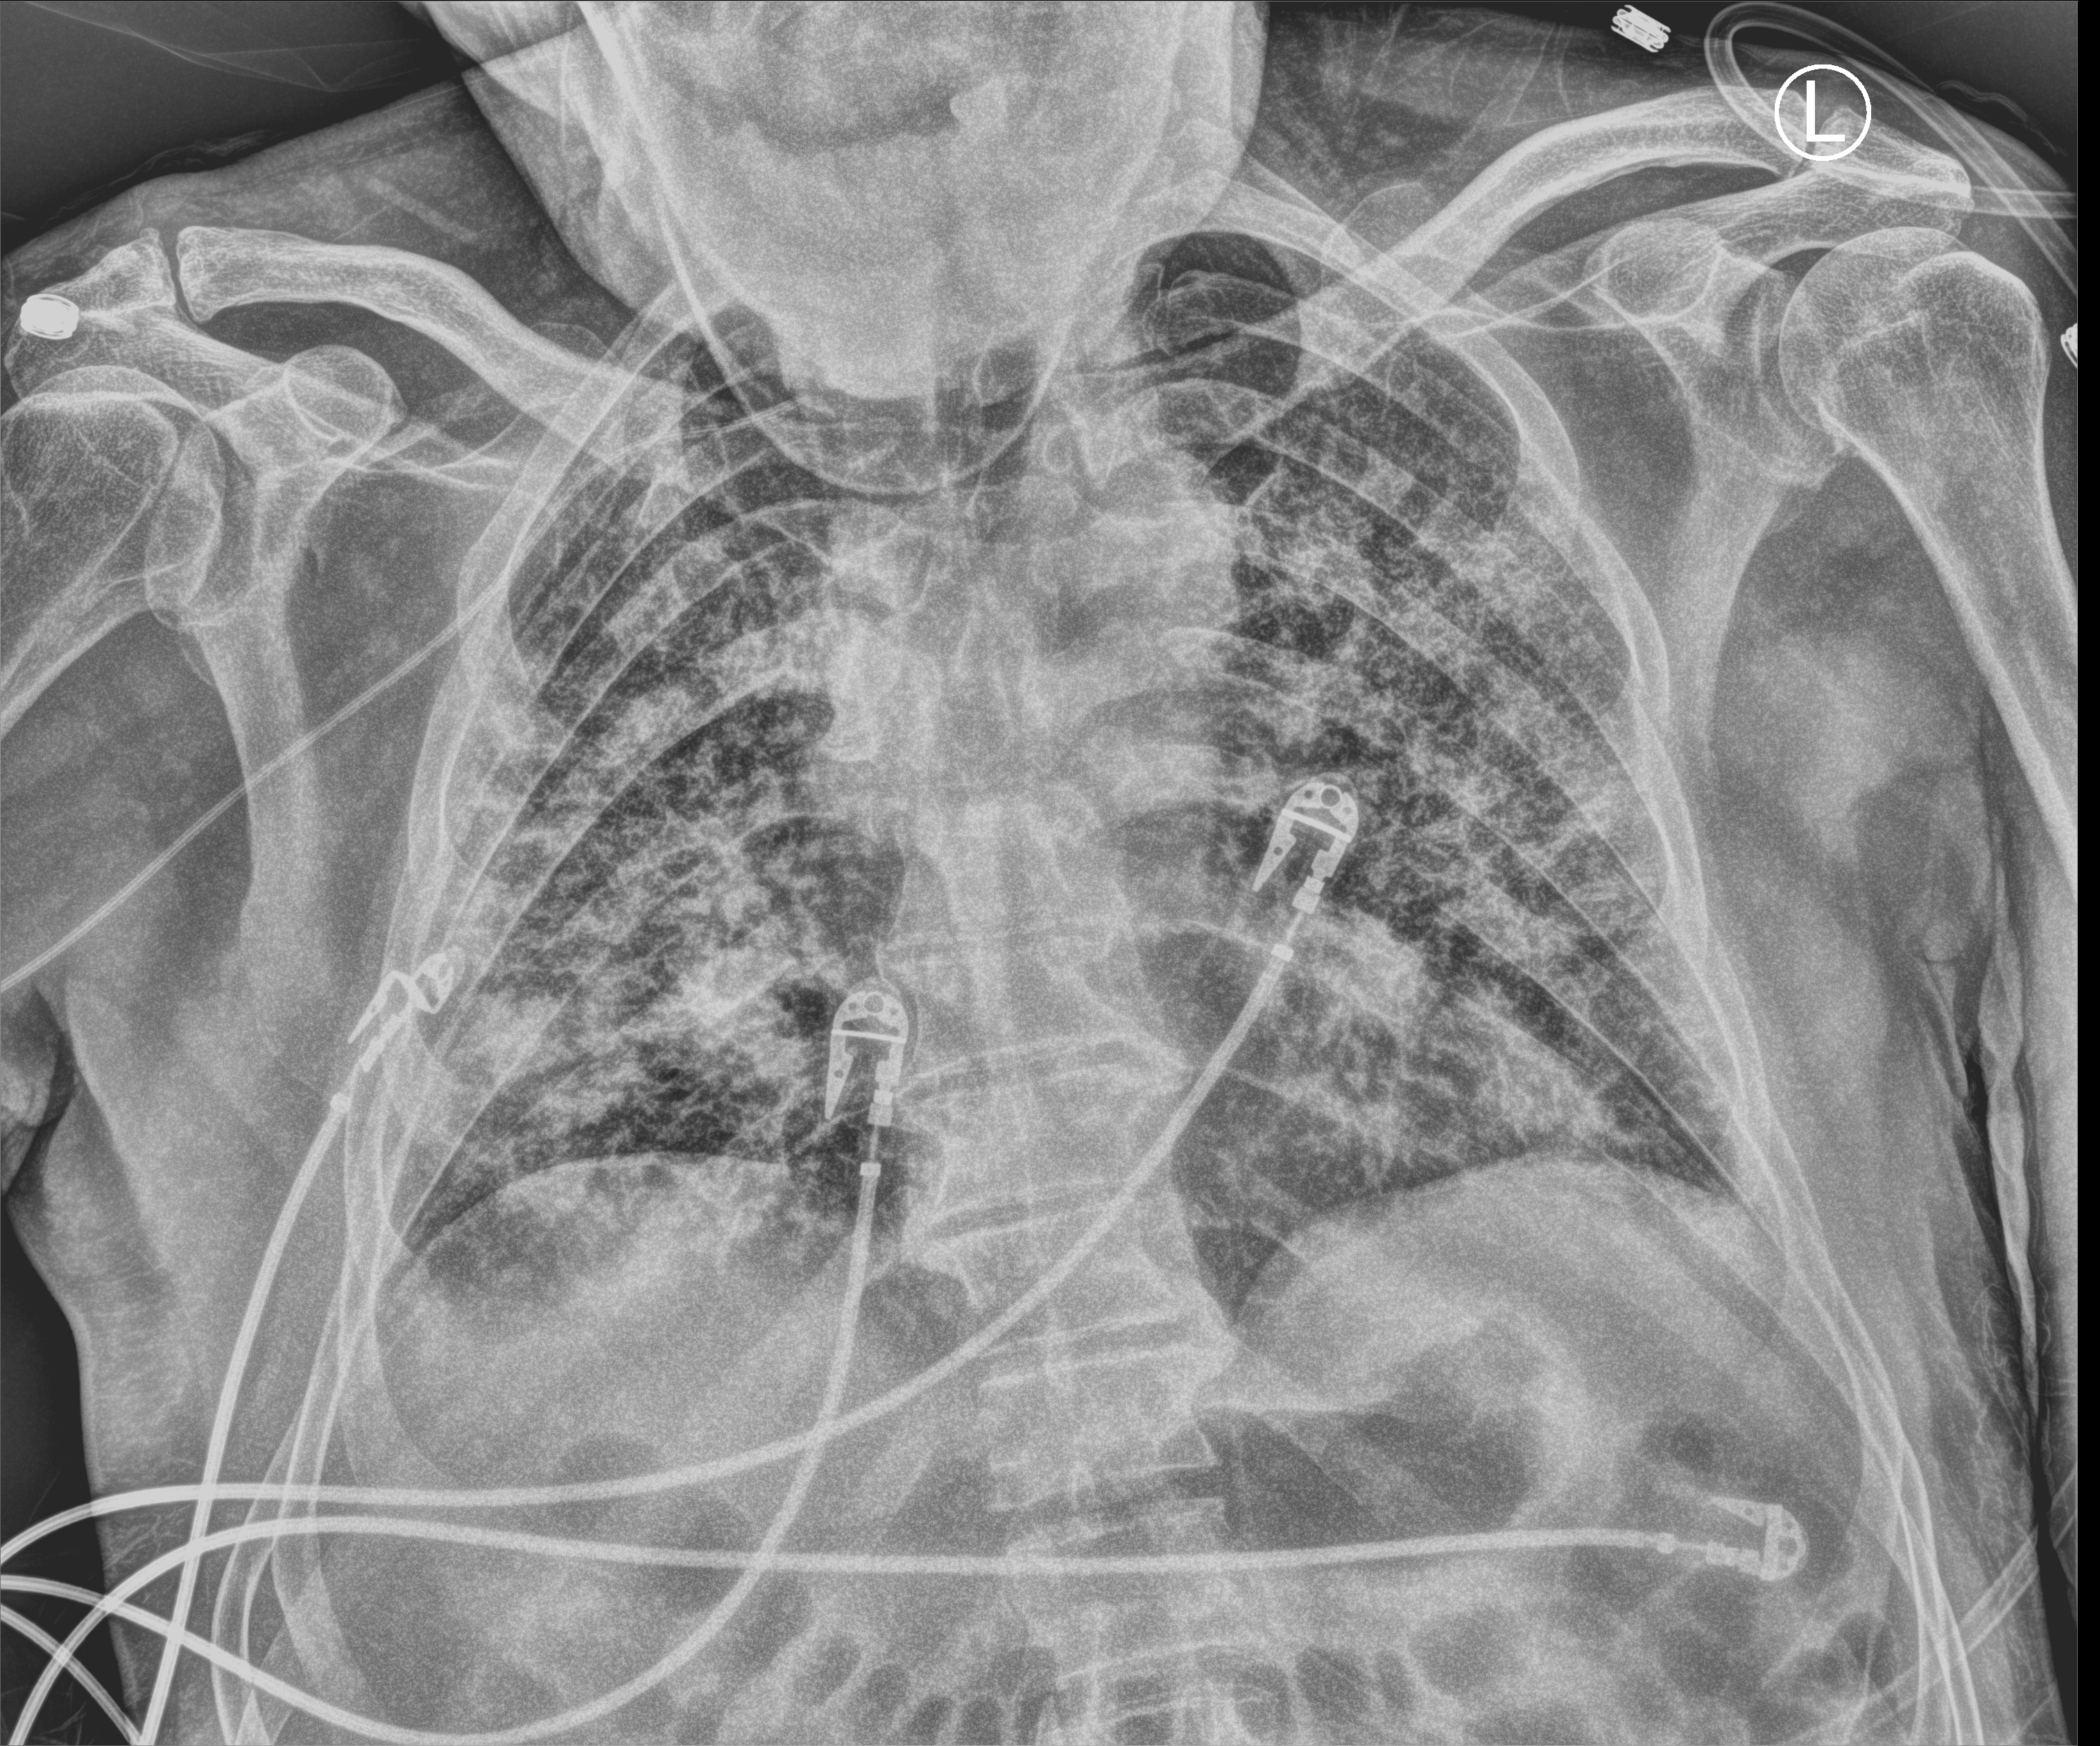
Chest X-ray (portable). Patient hospitalised with COVID-19; male, aged 60–74 years.
Admission-level facts for this patient (not findings on this image; timing relative to this image not recorded): admitted to intensive care during this hospital stay: yes; mechanically ventilated during this hospital stay: yes.